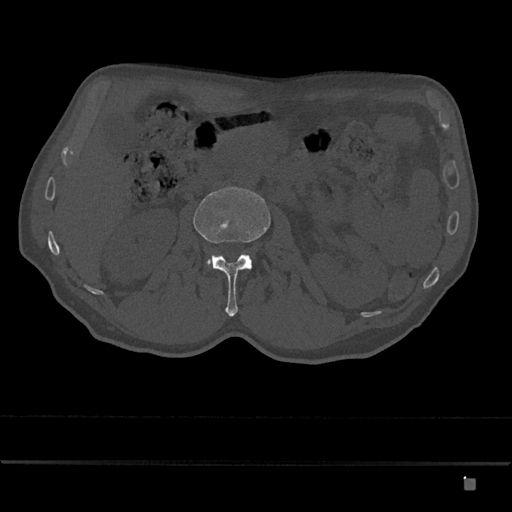
CT including the spine, one axial slice. Position 464 of 797 along the scan axis. Reconstruction kernel Br40s/3. 120 kVp. Bone window (W 1800 / L 400 HU). 0.5 mm slice thickness. 512 × 512 image matrix, field of view 390 × 390 mm. Patient: male, 72 years. From the clinical record (not read from this slice): primary cancer: prostate.
Outlined on this slice (semi-automatic segmentation, software-assisted and operator-edited):
- L2 vertebra: bounding box [x1, y1, x2, y2] px = [193, 187, 271, 317]
- L3 vertebra: [206, 259, 211, 265]